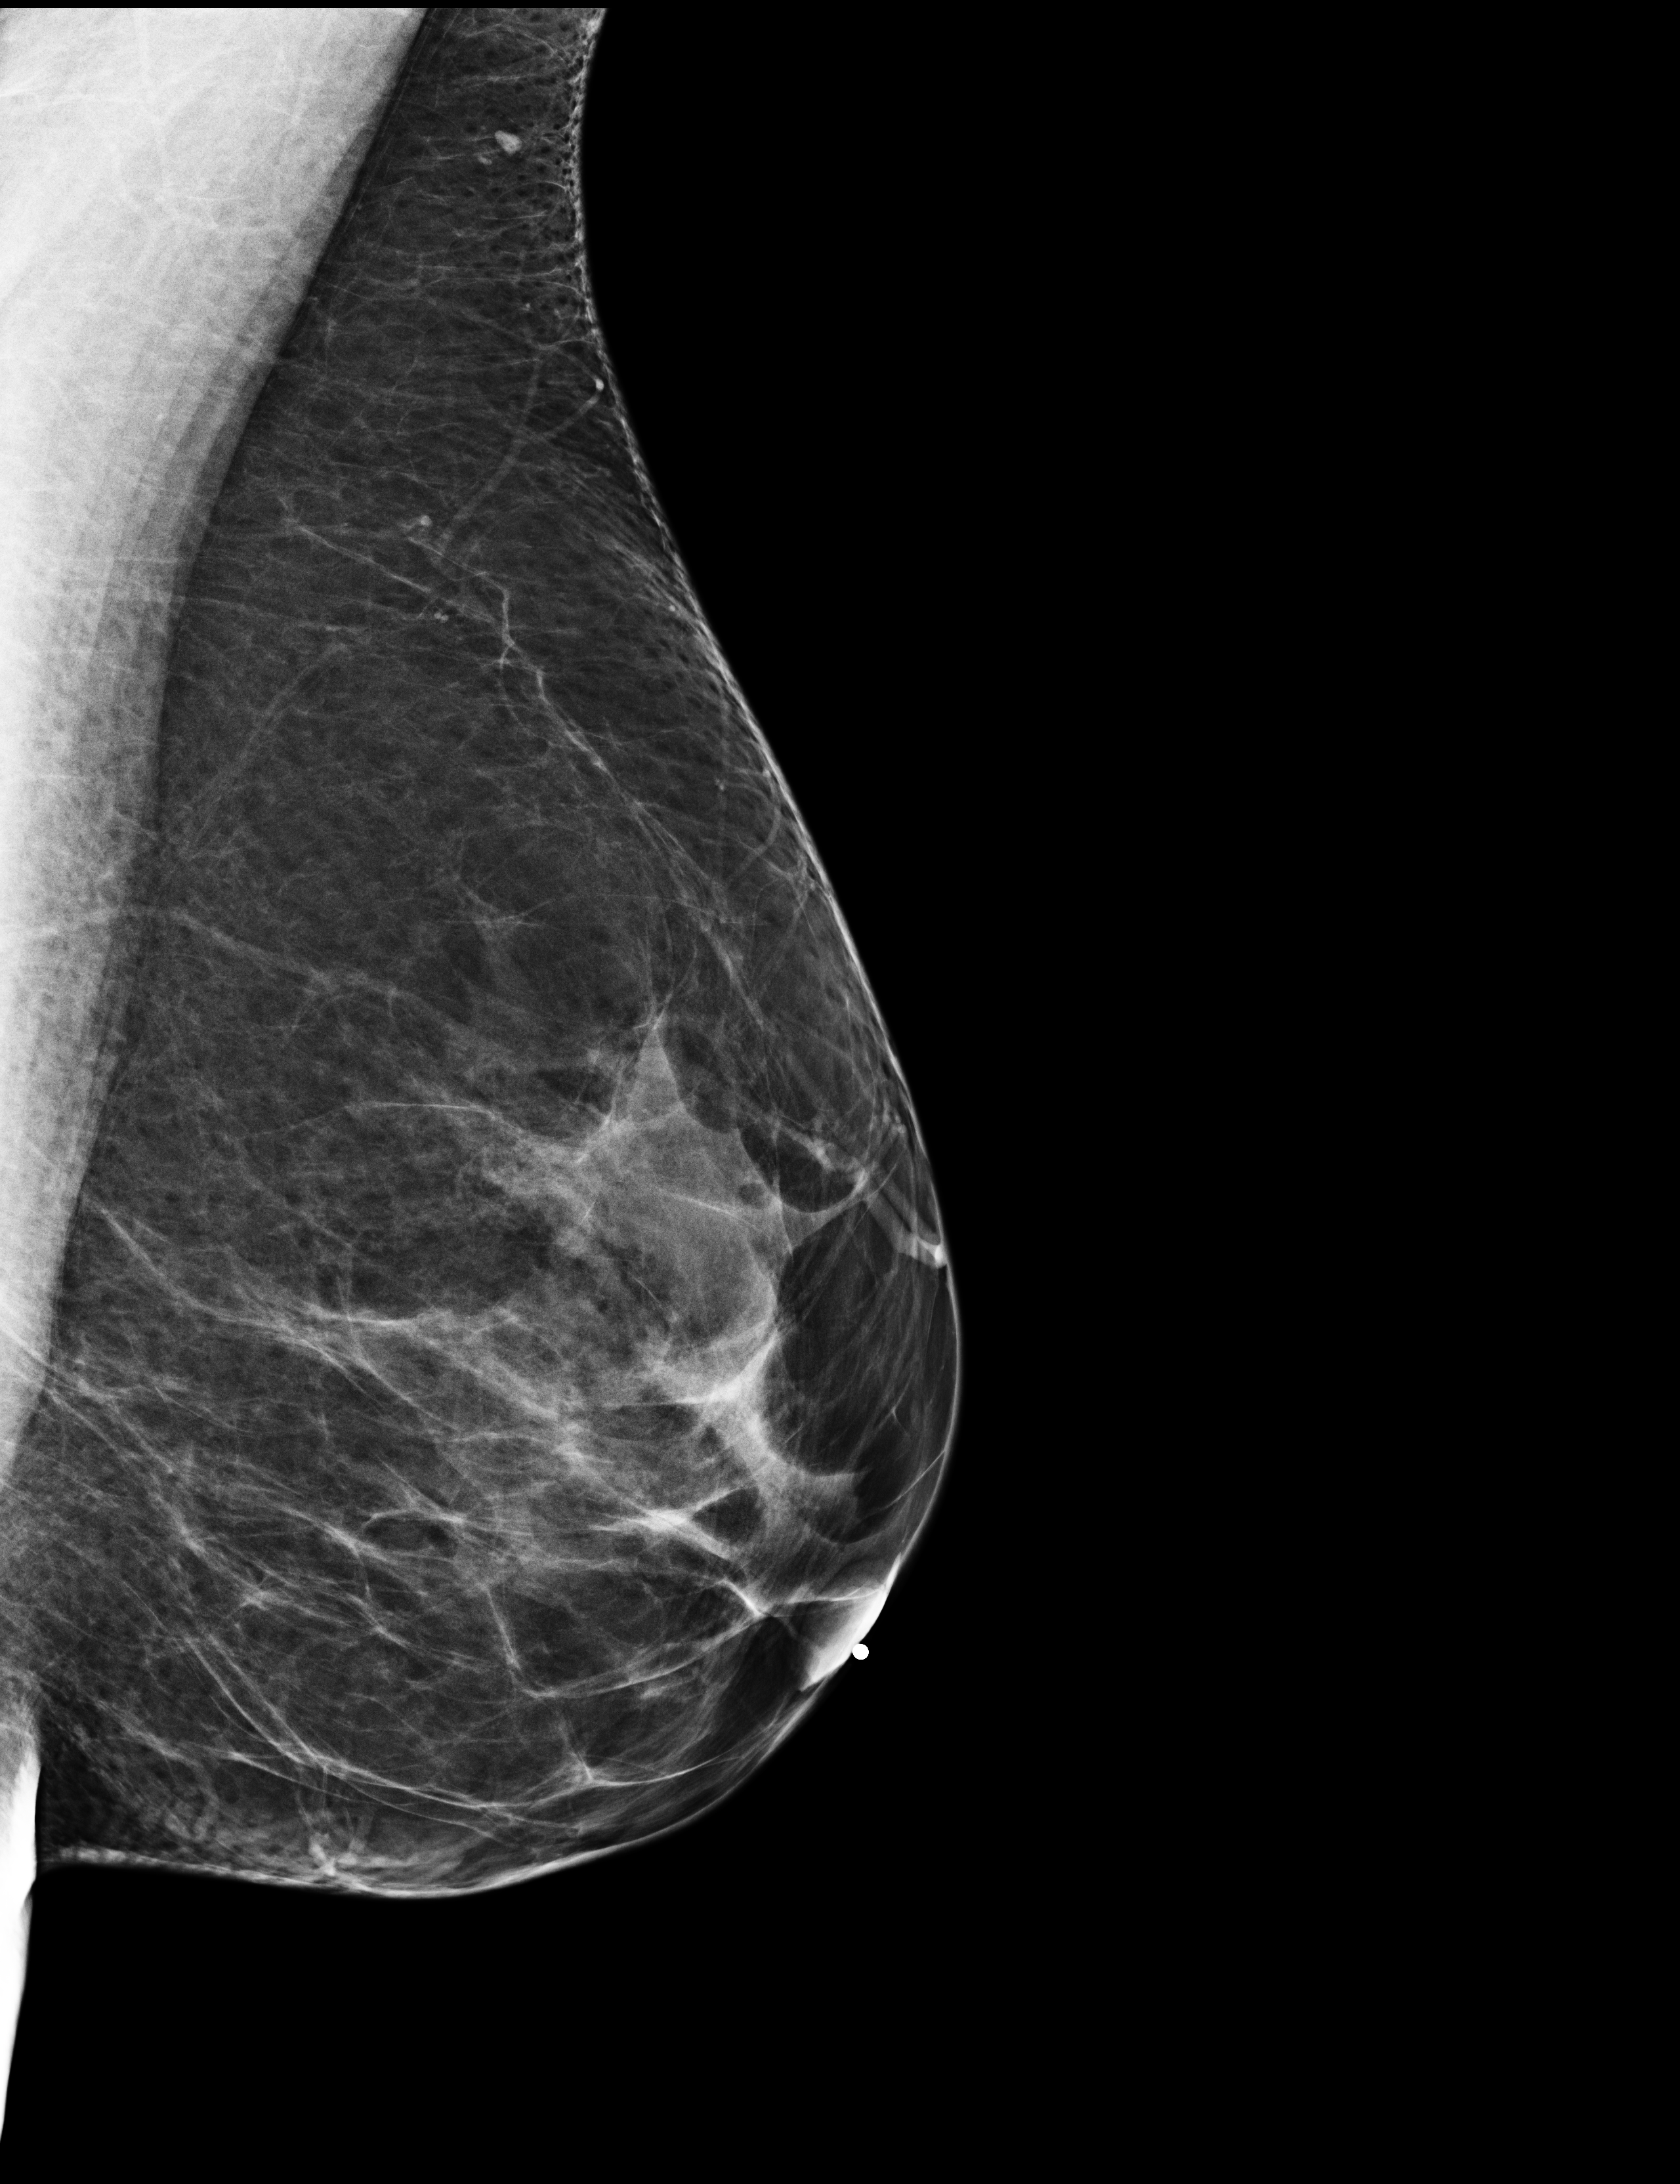
Annual screening mammography examination, compressed breast thickness 71 mm. Female patient, age 50 years.
Image type: full-field digital mammogram. Breast: left. Projection: medio-lateral oblique projection.